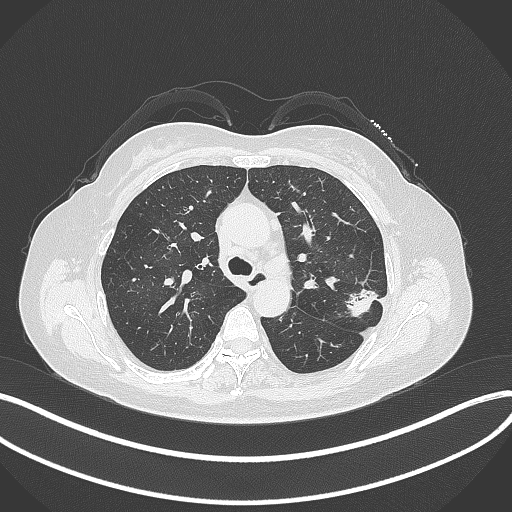
Chest CT, one axial slice. Position 220 of 319 along the scan axis. 120 kVp. Lung window (W 1500 / L -600 HU). 512 × 512 image matrix, field of view 400 × 400 mm. Patient: female, 60 years. Case-level facts recorded for this patient, not image findings: clinical TNM (as recorded): T1c N0 M0.
Annotated regions visible in this slice (bounding box drawn by a radiologist):
- lung tumour (recorded histology: adenocarcinoma): bounding box (x1, y1, x2, y2) in pixels: (344, 282, 384, 317)